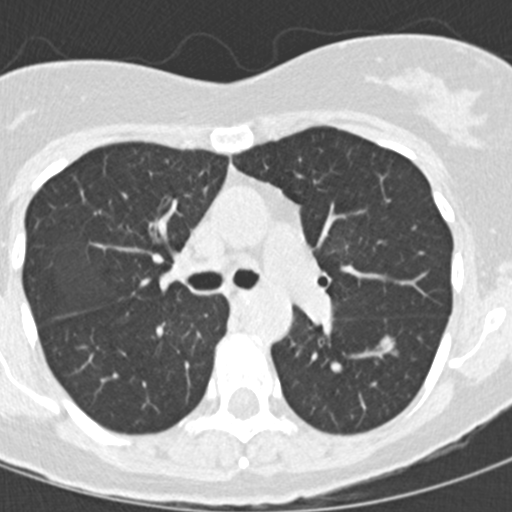
Low-dose screening chest CT, one axial slice. Slice 92 of 145 in the series (ordered by position). Lung window (W 1500 / L -600 HU). 512 × 512 image matrix, field of view 270 × 270 mm.
Structures marked on this image (expert manual segmentation):
- lesion 1 (tumor, lower lobe of left lung): bounding box [x1, y1, x2, y2] px = [380, 336, 394, 349]